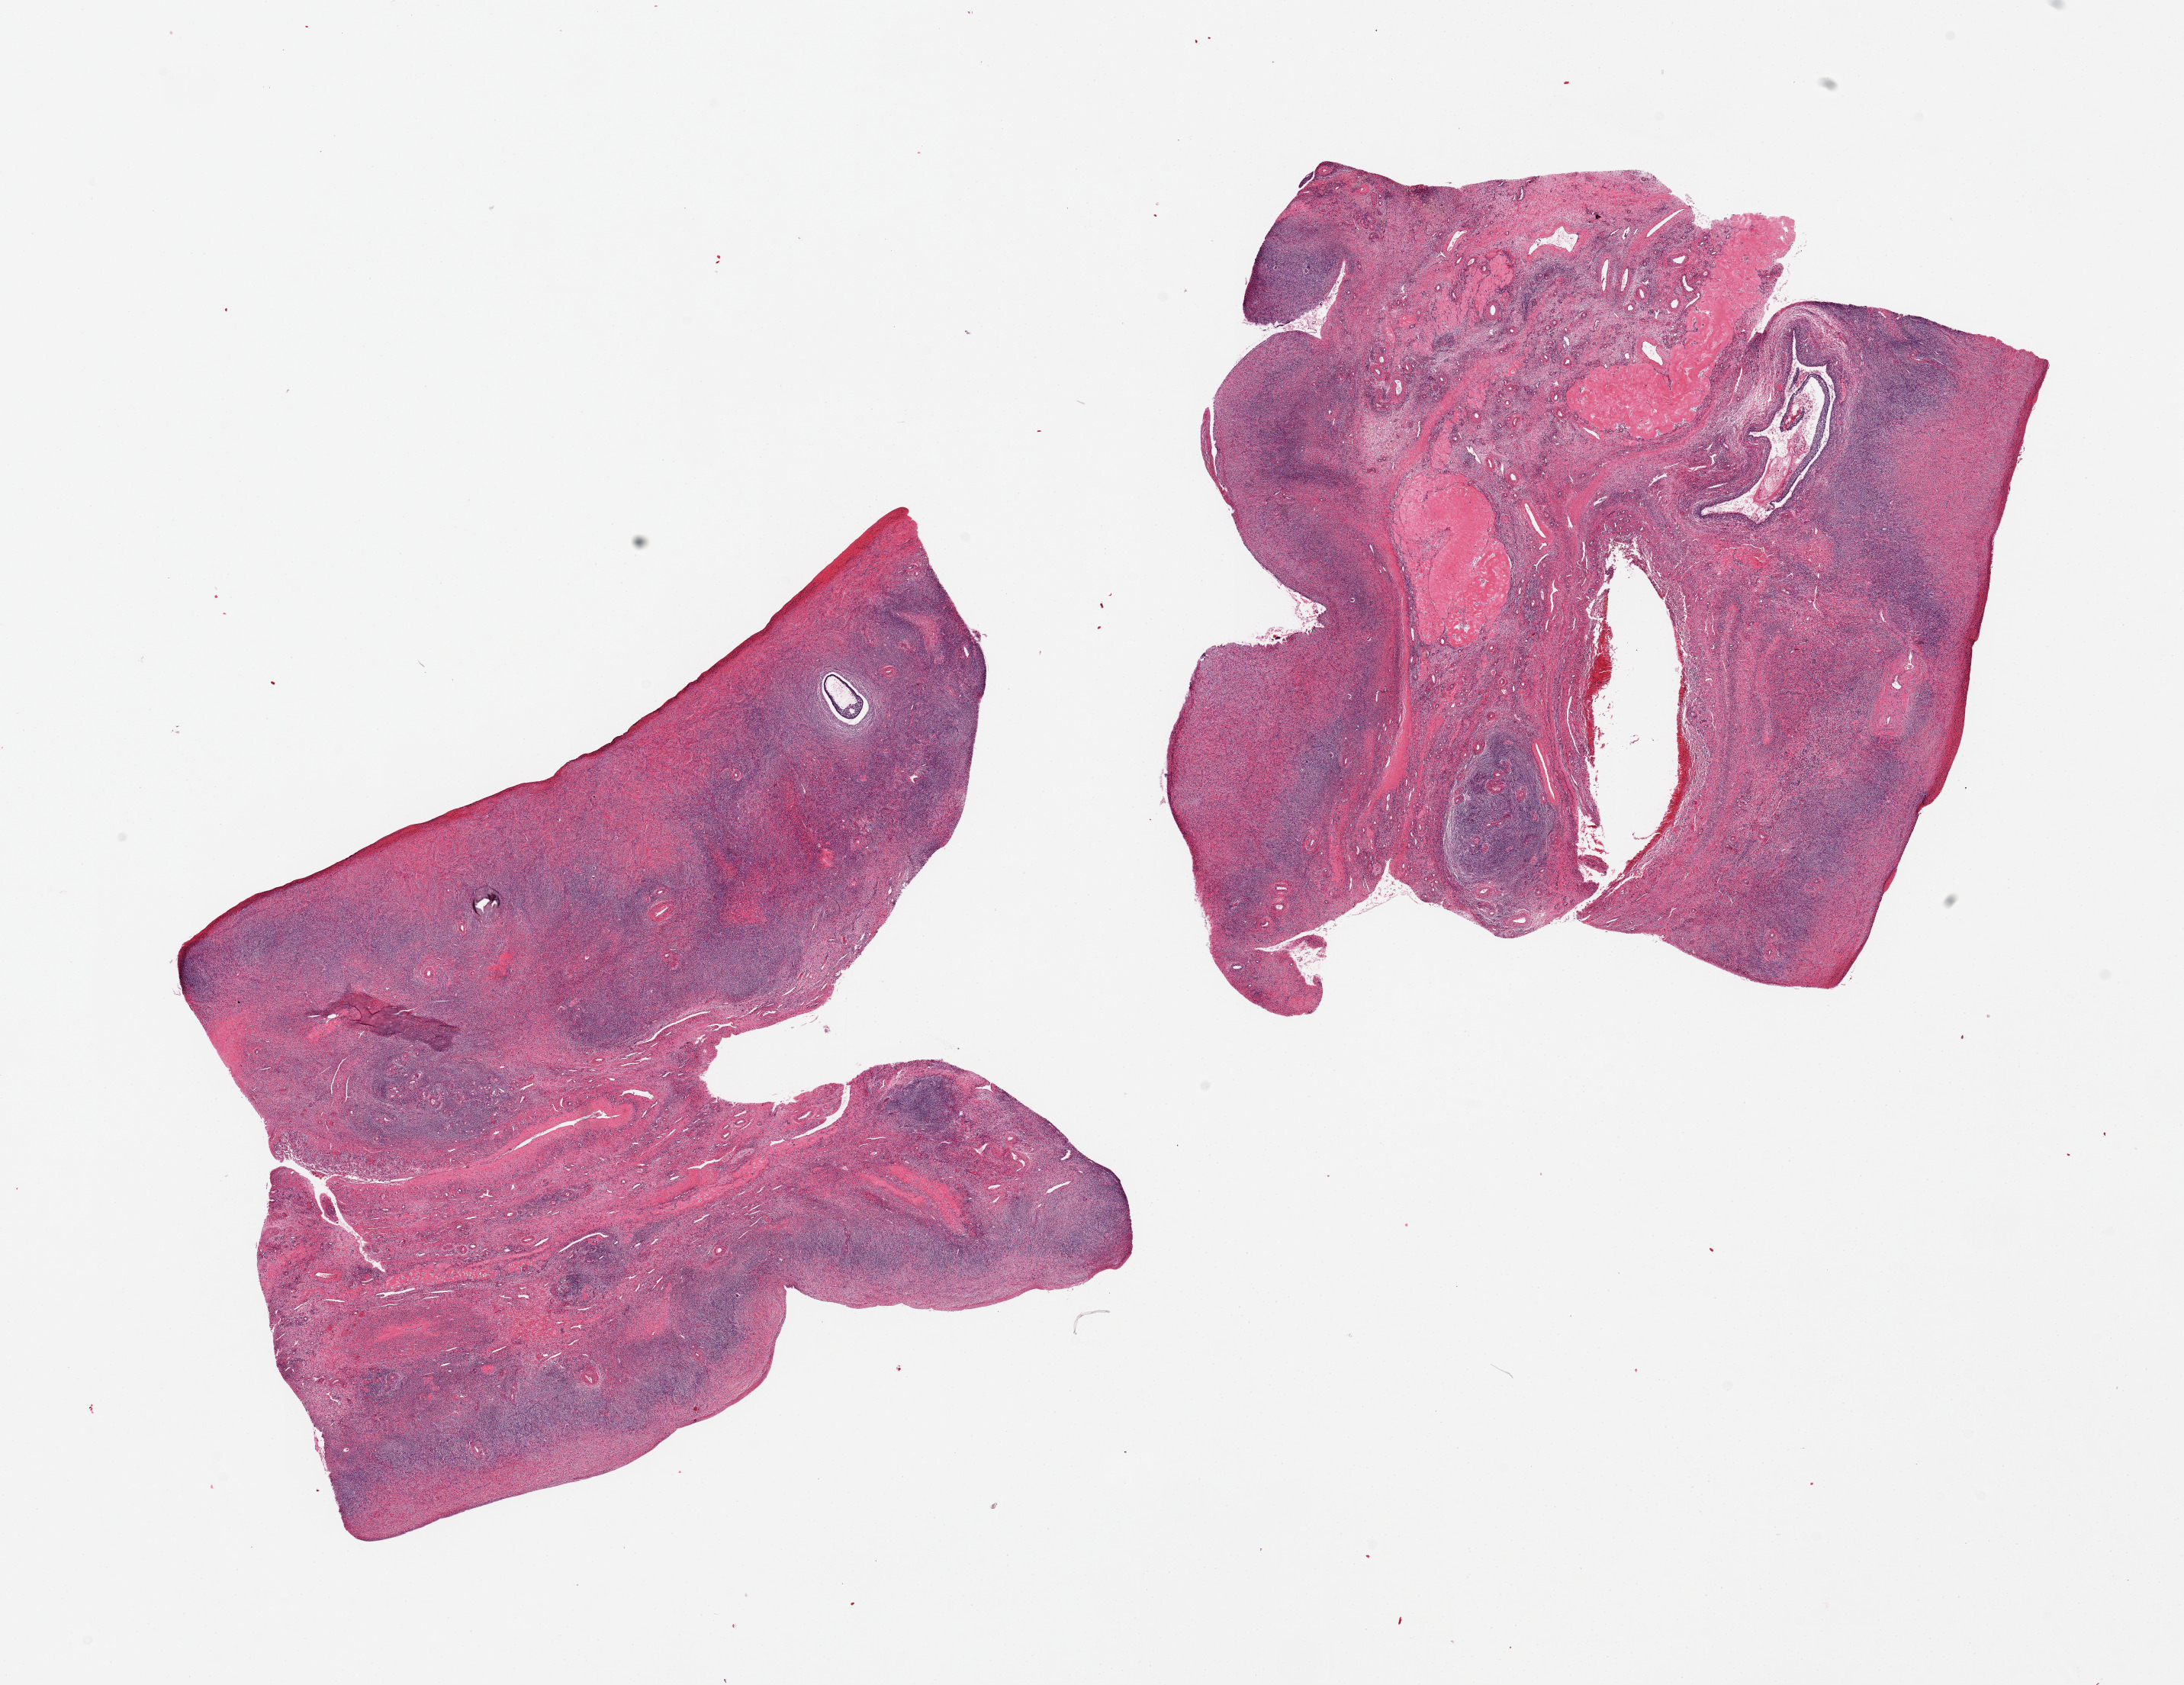
Whole-slide image, haematoxylin and eosin stain, brightfield, whole scanned area (about 22.6 x 17.5 mm, slide scanned at 20x) shown as a low-resolution overview, PAXgene-fixed paraffin-embedded (PFPE) section, target tissue: ovary, tissue donor sample. Donor: female.
Pathologist's review note for this sample: 2 pieces, involutional cortex, small (~1mm) follicular cyst.